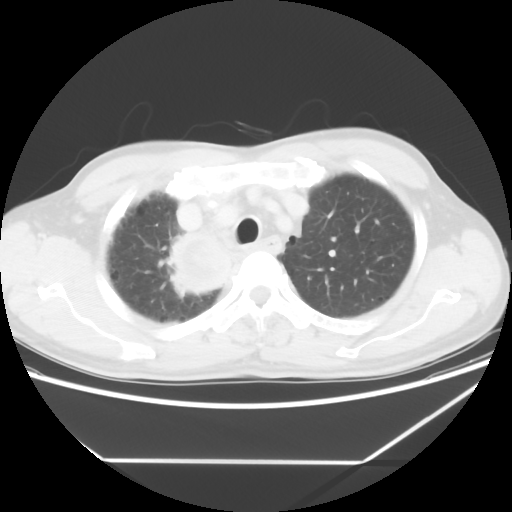
Chest CT, one axial slice. Reconstruction kernel STANDARD. Lung window (W 1500 / L -600 HU). 5 mm slice thickness. 512 × 512 image matrix. Patient: male, 58 years. Case-level facts recorded for this patient, not image findings: clinical TNM (as recorded): T2 N2 M0.
Outlined on this slice (bounding box drawn by a radiologist):
- lung tumour (recorded histology: squamous cell carcinoma): bounding box <165,230,234,301> (left, top, right, bottom; pixels)